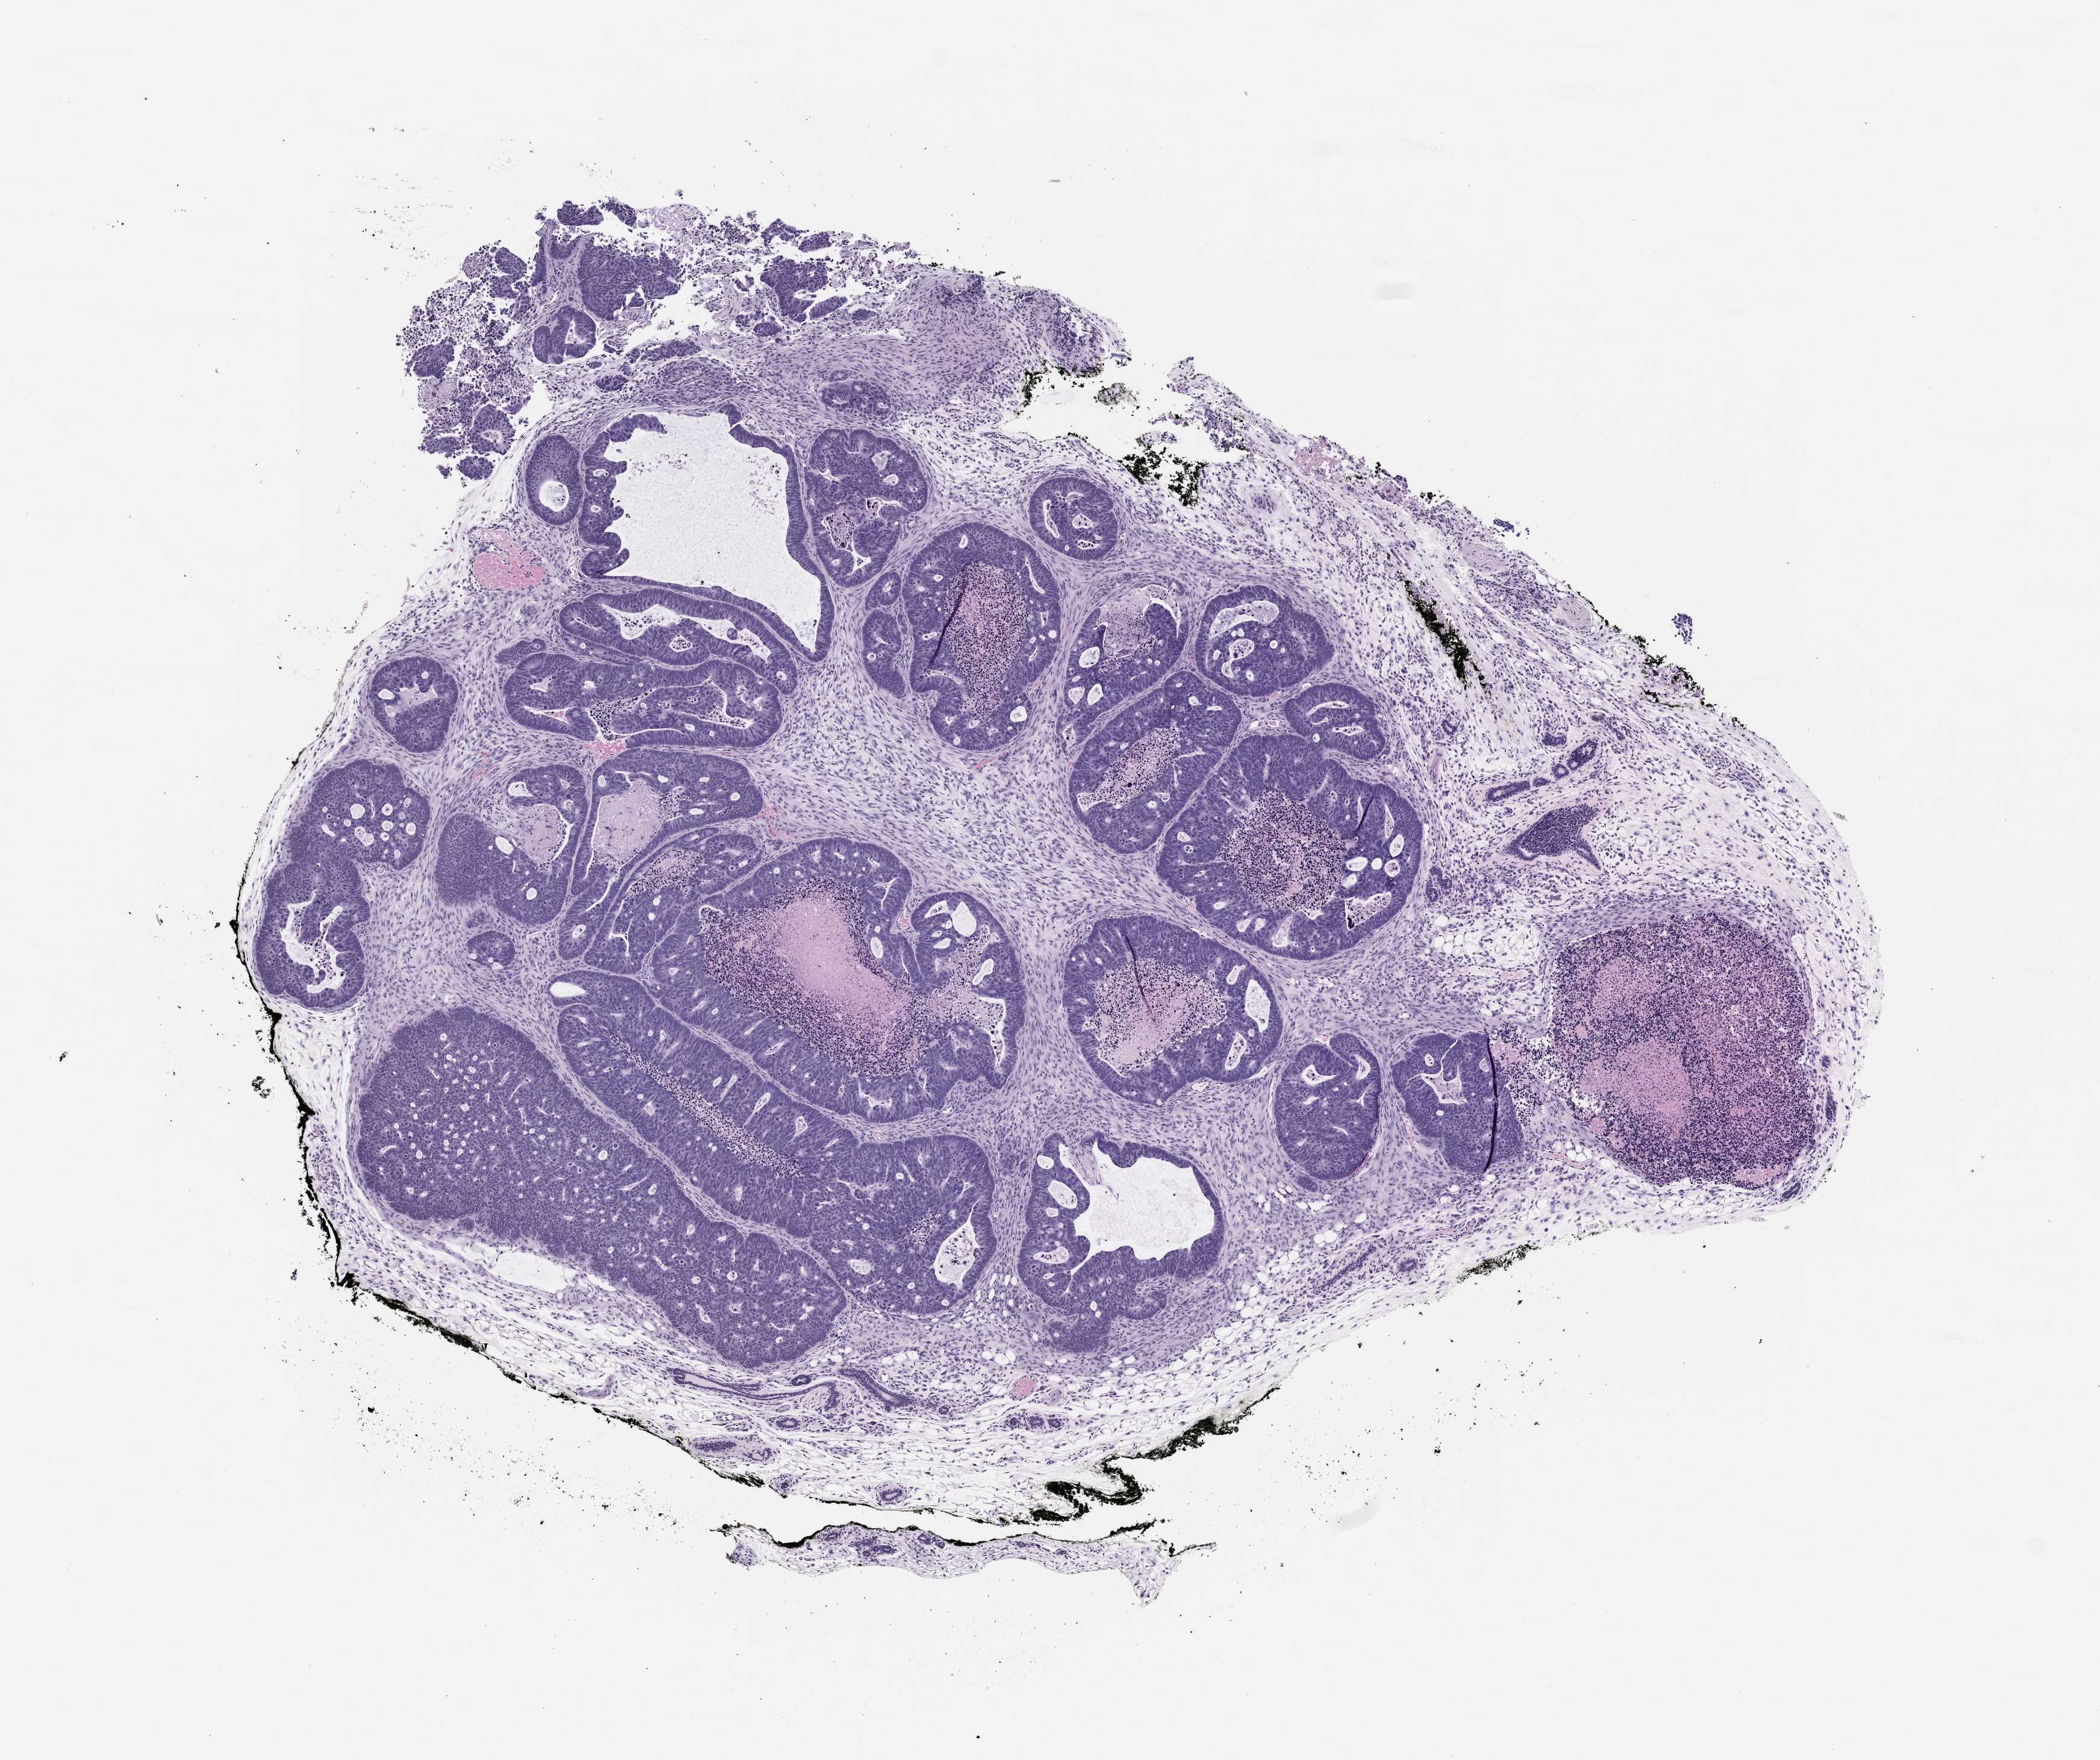
Haematoxylin and eosin whole-slide image of a patient-derived xenograft (PDX) tumor grown in a mouse, passage 0, a low-resolution overview of the entire scanned area, about 7.0 x 5.9 mm, FFPE section, originating tumor site category: colon.
Originating patient diagnosis: Colon Adenocarcinoma.